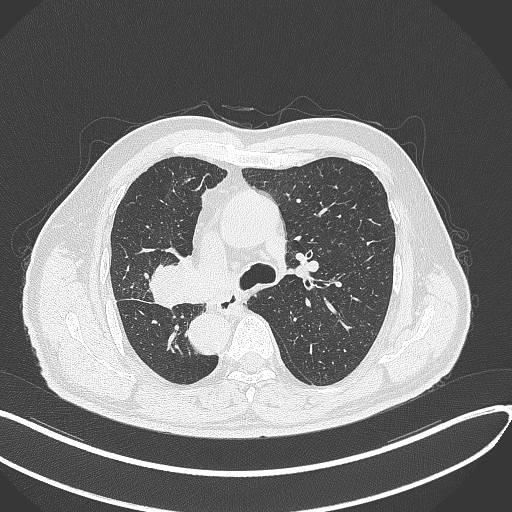
Chest CT, one axial slice; position 197 of 300 along the scan axis; reconstruction kernel B70f; 120 kVp; lung window (W 1500 / L -600 HU); 1 mm slice thickness; 512 × 512 image matrix, field of view 400 × 400 mm. Male patient, age 67 years. From the clinical record (not read from this slice): clinical TNM (as recorded): T2a N0 M0.
Structures marked on this image (bounding box drawn by a radiologist):
- lung tumour (recorded histology: squamous cell carcinoma): bounding box (x1, y1, x2, y2) in pixels: (143, 257, 199, 312)